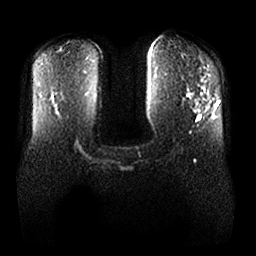
Breast MRI, one axial slice. Position 11 of 25 along the scan axis. Diffusion-weighted series; image 2 of 4 stored at this slice position (different b-values; order by instance number). 1.5 T. 4 mm slice thickness. 256 × 256 image matrix, field of view 370 × 370 mm. Female patient.
Annotated regions visible in this slice (manually delineated by an expert):
- tumour on diffusion-weighted imaging: box from (x=195, y=102) to (x=199, y=106) px